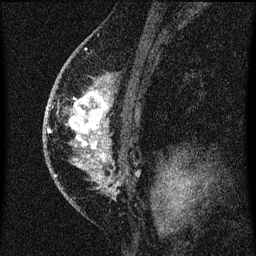
Breast MRI (dynamic contrast-enhanced), one sagittal slice. Position 44 of 60 along the scan axis. Dynamic contrast-enhanced series, image 2 of 3 at this slice position (ordered by acquisition). 1.5 T. TE 4.2 ms, TR 8 ms. 2 mm slice thickness. 256 × 256 image matrix, field of view 180 × 180 mm. Female patient, age 46 years.
Annotated regions visible in this slice (semi-automatically segmented with operator editing):
- analysis volume of interest (the breast-tissue region the enhancement analysis was run in; not a lesion): bounding box (x1, y1, x2, y2) in pixels: (54, 68, 114, 195)
- tumour enhancement mask (voxels above the 70 % enhancement threshold inside the analysis volume of interest): (69, 92, 109, 167)